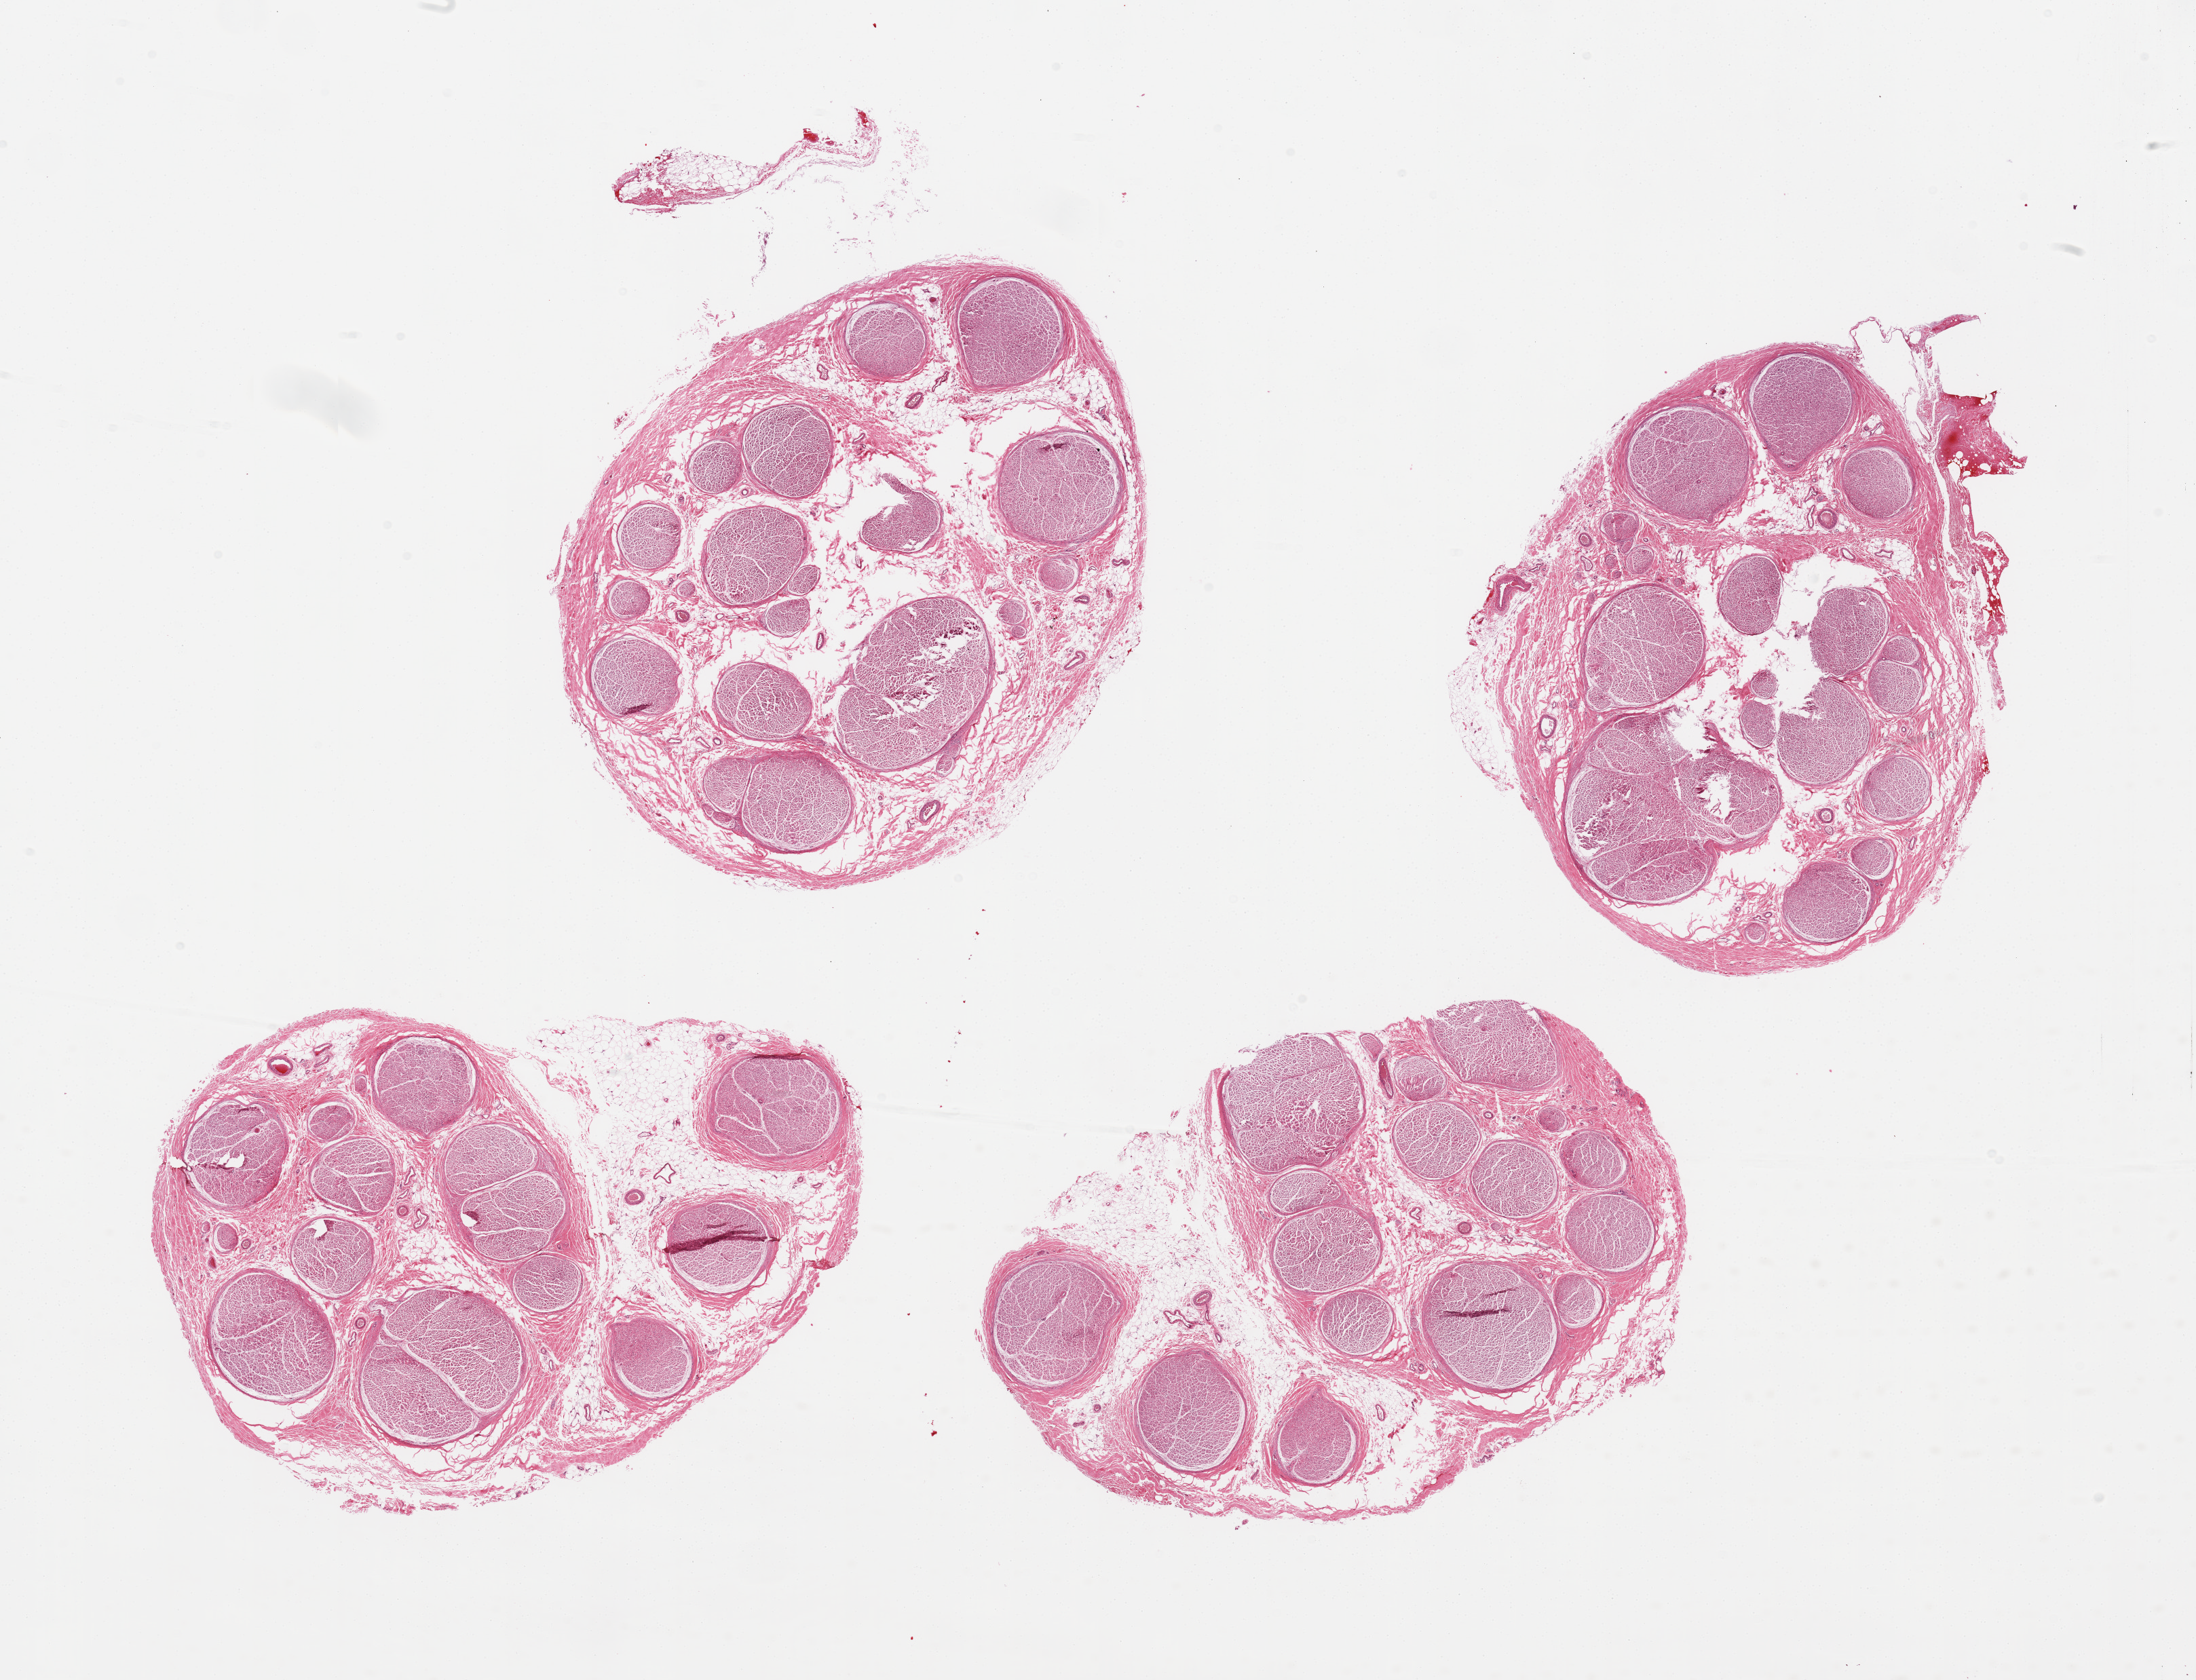
Digitized haematoxylin and eosin-stained section, brightfield — low-resolution overview of the scanned area, about 25.6 x 19.6 mm, PAXgene-fixed, paraffin-embedded tissue, sampled site (target tissue): tibial nerve, donor tissue sample.
Pathologist's review note for this sample: 4 pieces, 10 to 20% internal fat.